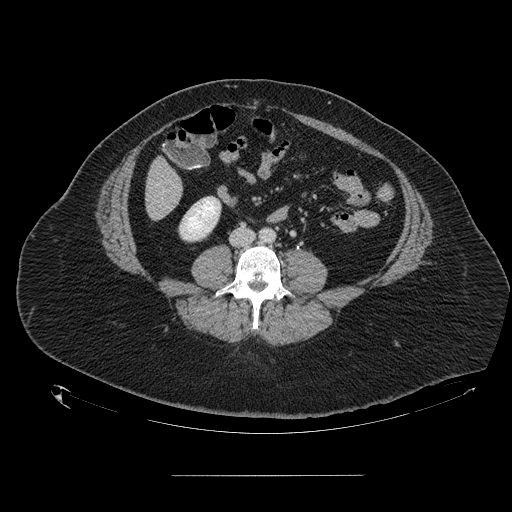
Contrast-enhanced abdominal CT, one axial slice. Position 20 of 164 along the scan axis. 120 kVp. Intravenous contrast given. Soft-tissue window (W 400 / L 40 HU). 2.5 mm slice thickness. 512 × 512 image matrix, field of view 495 × 495 mm. Female patient, age 52 years. From the clinical record (not read from this slice): diagnosis: colorectal cancer liver metastases, imaged before liver resection; multiple liver metastases: yes.
Outlined on this slice (outlined manually by an expert reader):
- liver: bounding box (x1, y1, x2, y2) in pixels: (146, 159, 182, 219)